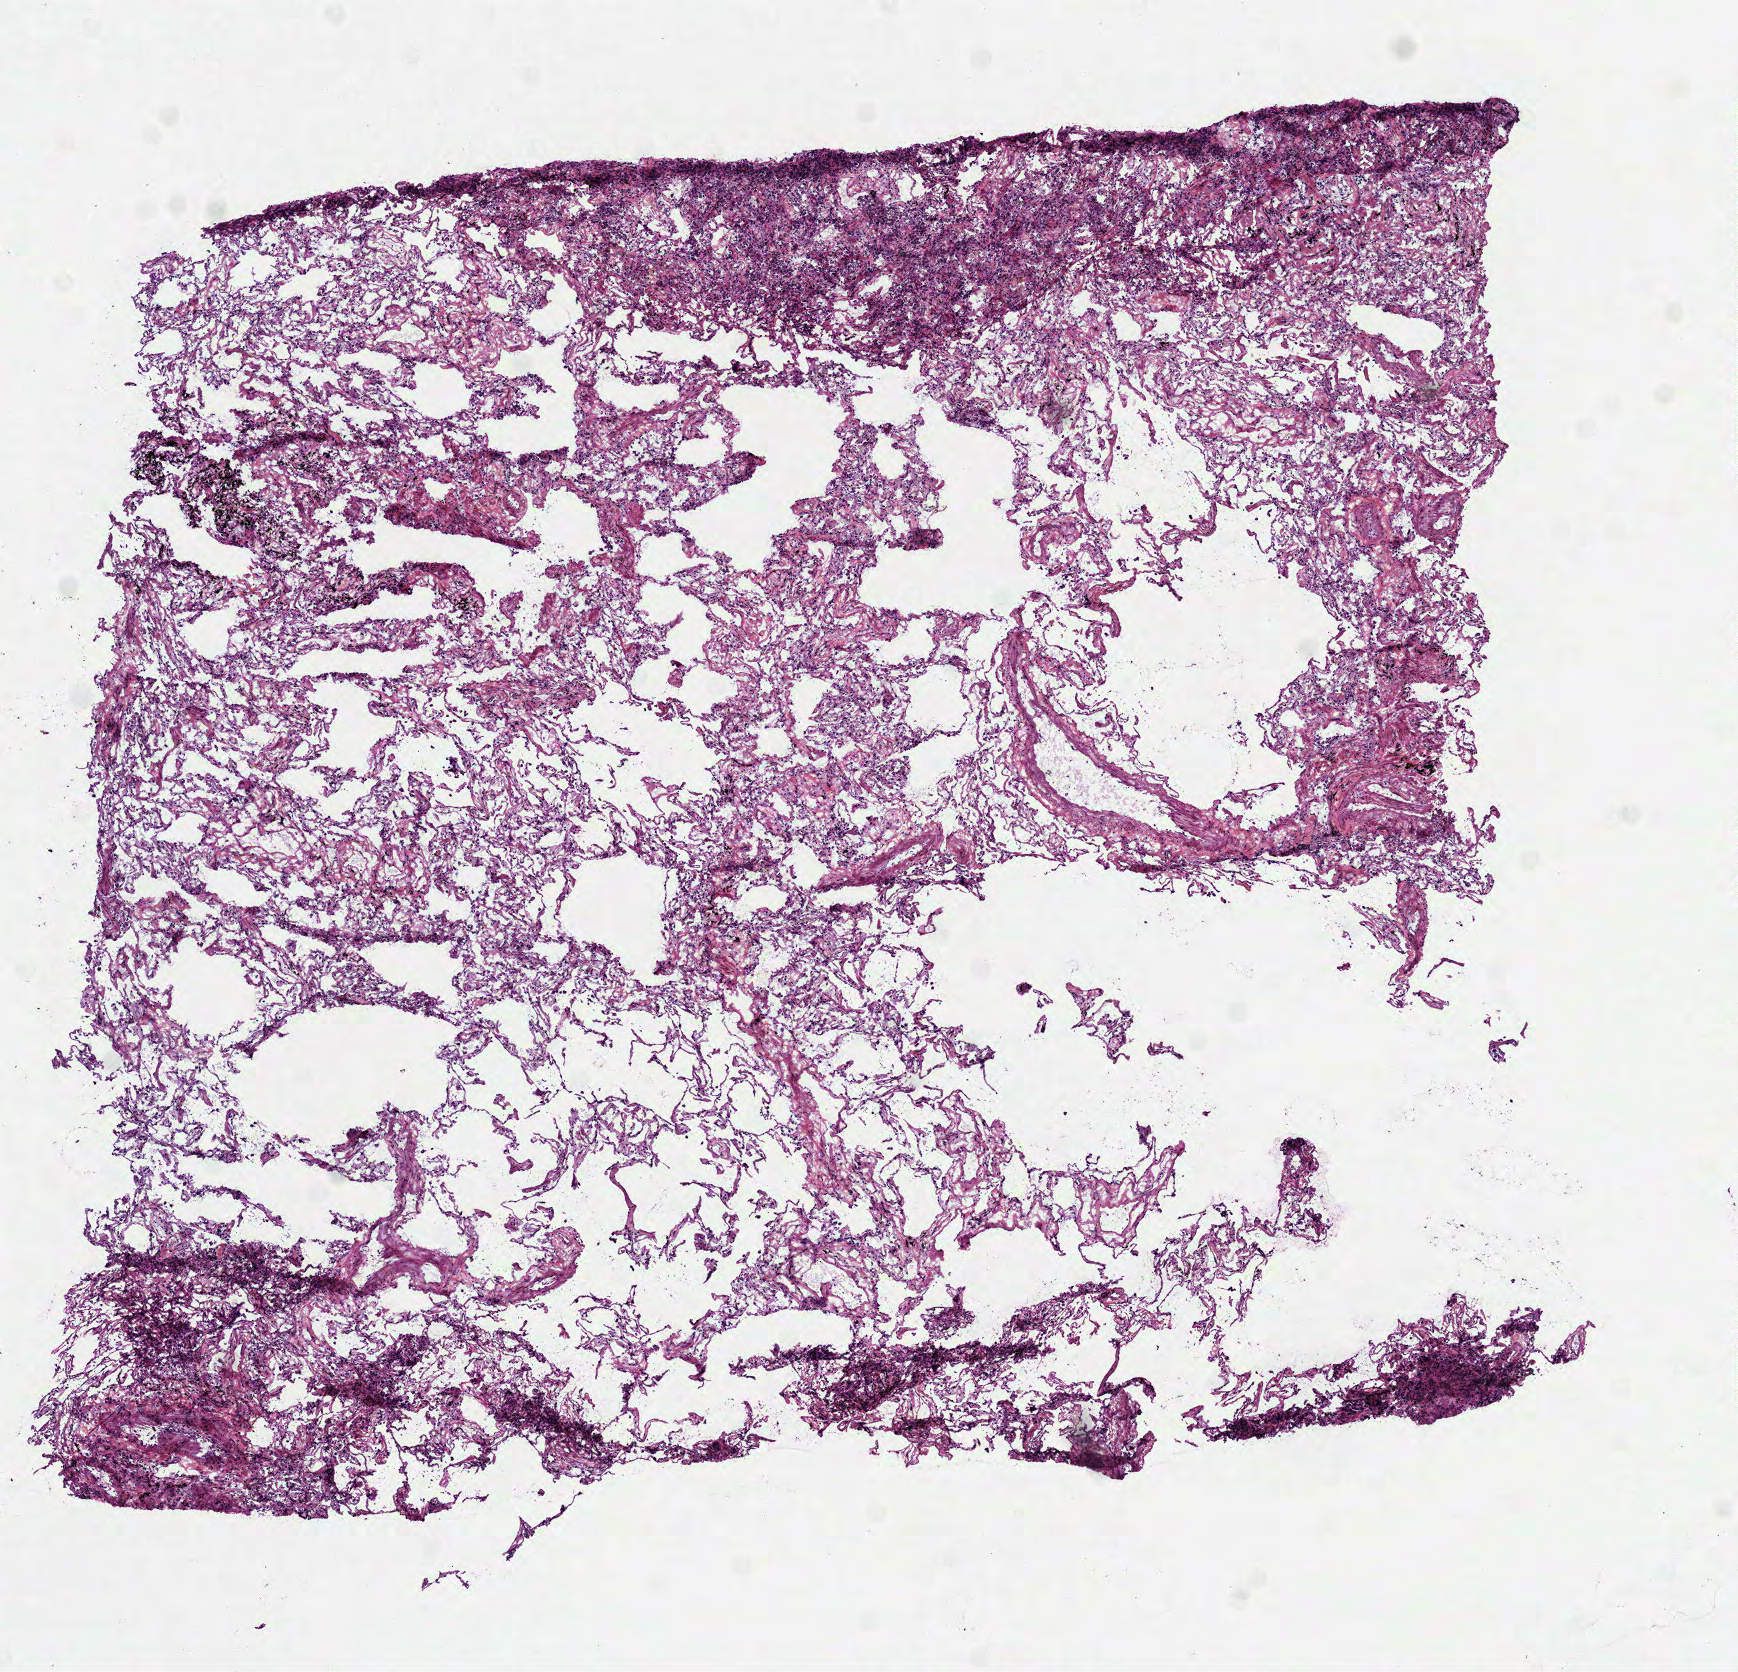
Whole-slide histology image, H&E — a low-resolution overview of the entire scanned area, about 7.0 x 6.7 mm (from a 40x scan). Frozen section from the top of the tissue portion. Lung, solid tissue normal (non-tumour tissue) sample. Male, age 84 years at initial diagnosis.
This section: solid tissue normal sample (biorepository sample class). Patient diagnosis: Squamous cell carcinoma, NOS (lower lobe, lung).